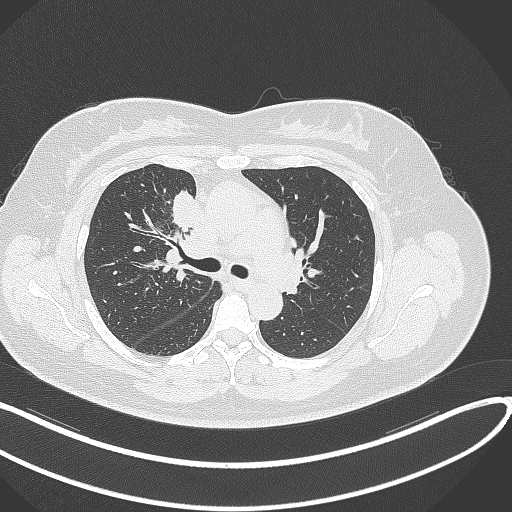
Chest CT, one axial slice. Slice 178 of 303 in the series (ordered by position). Reconstruction kernel B70f. 120 kVp. Lung window (W 1500 / L -600 HU). 1 mm slice thickness. 512 × 512 image matrix. Female patient, age 46 years. Case-level facts recorded for this patient, not image findings: clinical TNM (as recorded): T2a N1 M0.
Annotated regions visible in this slice (rectangle marked by the reading radiologist):
- lung tumour (recorded histology: adenocarcinoma): bounding box (x1, y1, x2, y2) in pixels: (165, 189, 204, 237)